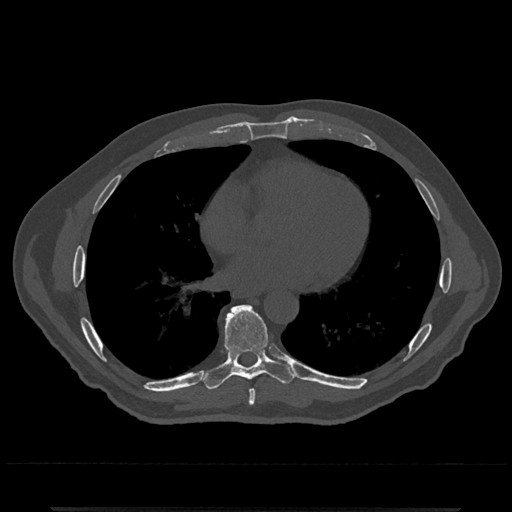
CT including the spine, one axial slice. Position 676 of 797 along the scan axis. Reconstruction kernel Br40s/3. Bone window (W 1800 / L 400 HU). 0.5 mm slice thickness. 512 × 512 image matrix, field of view 393 × 393 mm. Male patient, age 67 years. From the clinical record (not read from this slice): primary cancer: prostate.
Outlined on this slice (semi-automatic segmentation, software-assisted and operator-edited):
- T7 vertebra: box from (x=248, y=389) to (x=256, y=406) px
- T8 vertebra: (x=202, y=305)–(x=295, y=390)